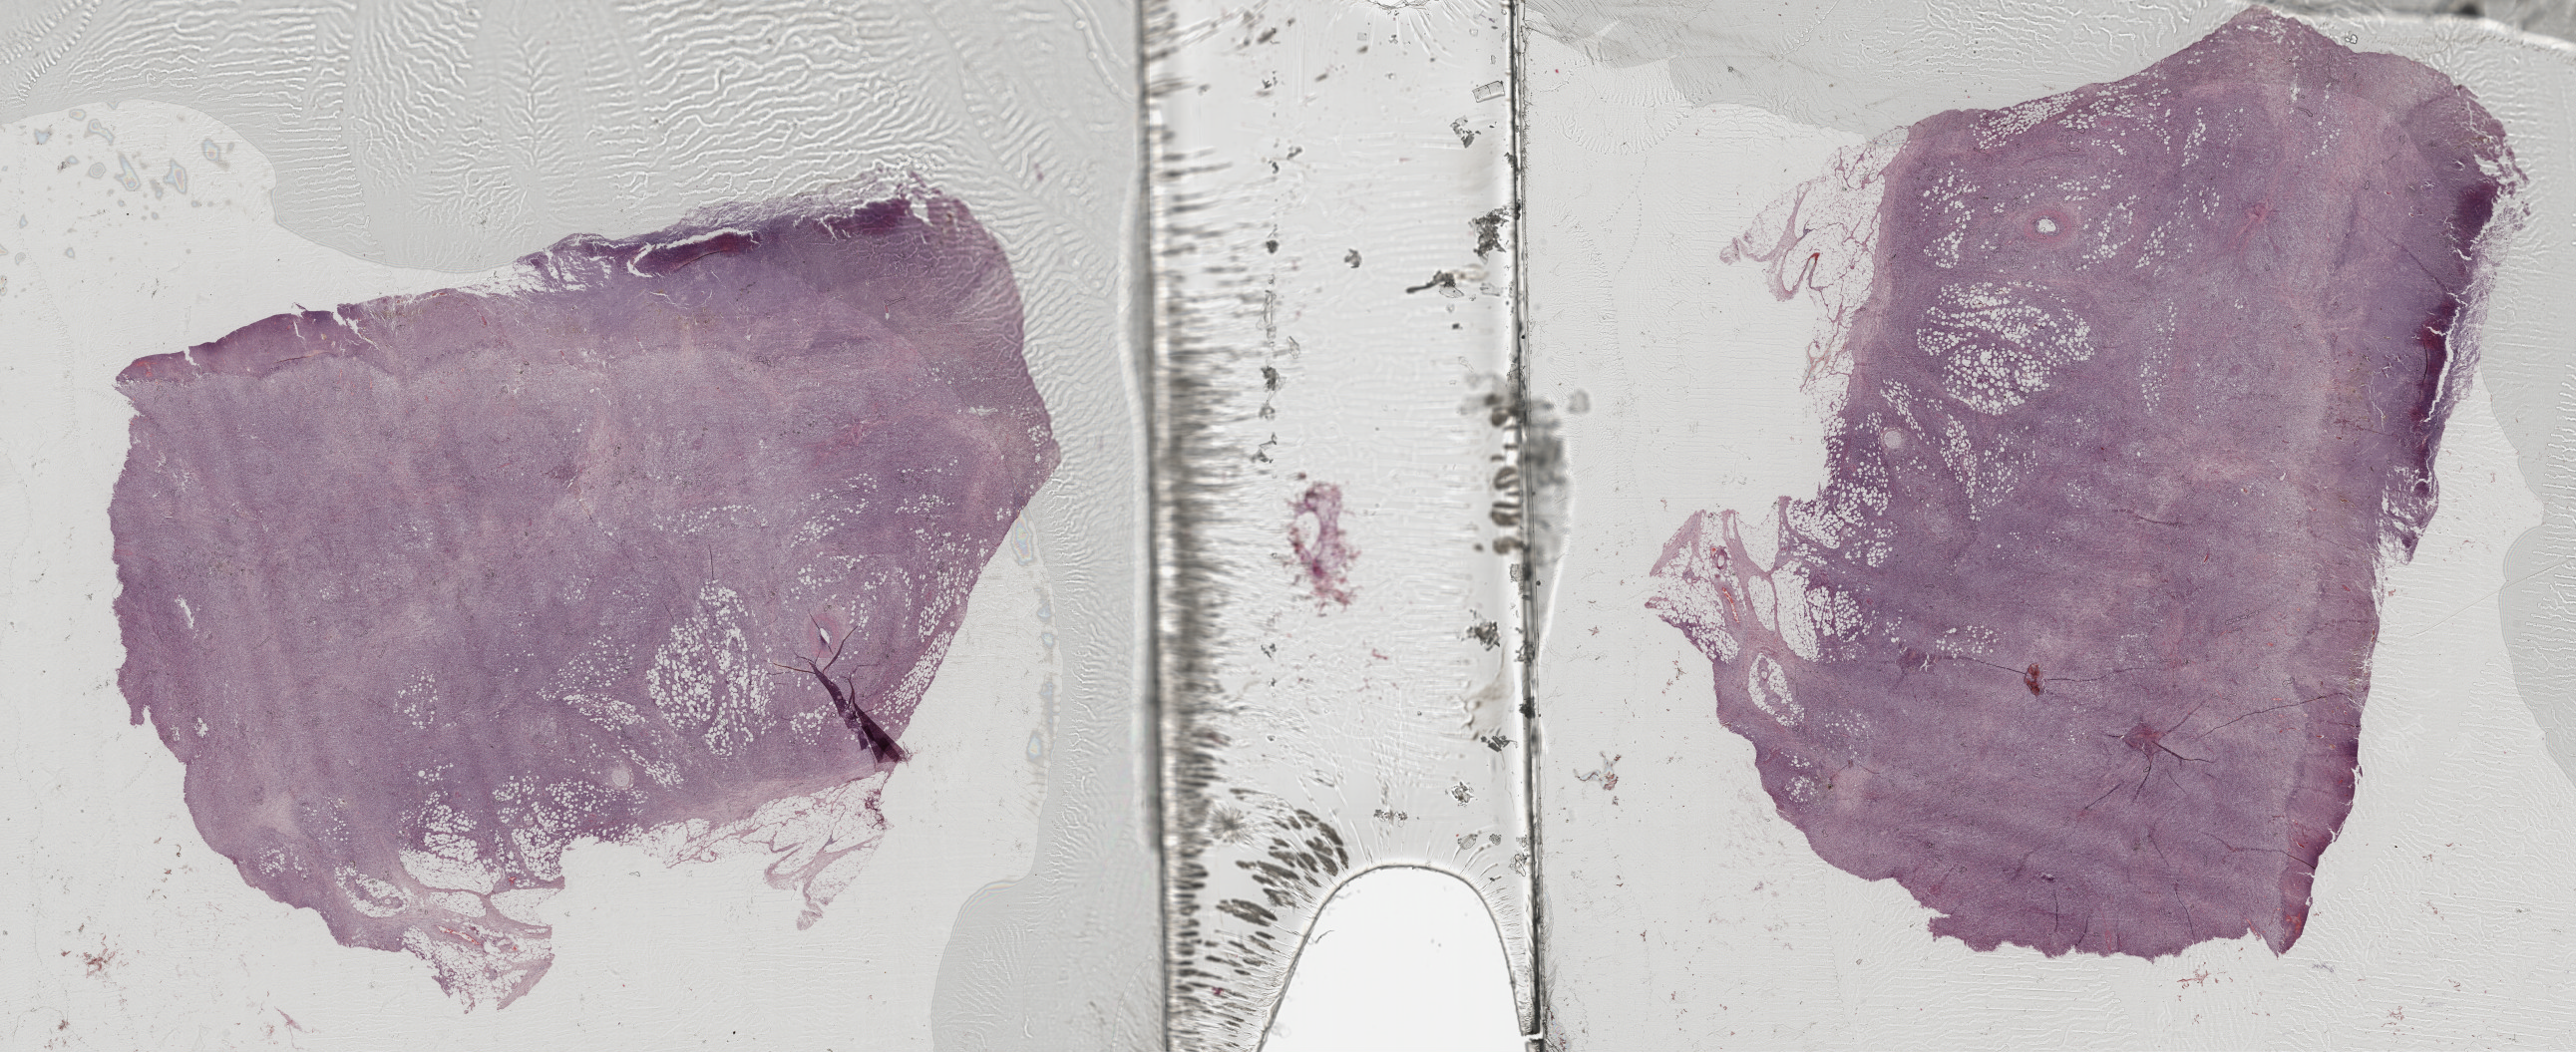
Whole-slide histology image, H&E — shown as a low-resolution overview of the whole scanned area (about 41.8 x 17.1 mm, acquisition: 40x scan); formalin-fixed paraffin-embedded (FFPE) diagnostic section; lymphoid tissue, primary tumour sample. Male, age 55 years at initial diagnosis.
• diagnosis: Diffuse large B-cell lymphoma, NOS (stomach, NOS)